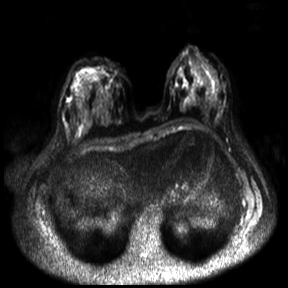
Breast MRI, one axial slice; position 13 of 30 along the scan axis; diffusion-weighted series; image 2 of 4 stored at this slice position (different b-values; order by instance number); 3 T; 4 mm slice thickness; 288 × 288 image matrix, field of view 360 × 360 mm. Female patient.
Outlined on this slice (expert manual segmentation):
- tumour on diffusion-weighted imaging: box from (x=69, y=96) to (x=72, y=103) px